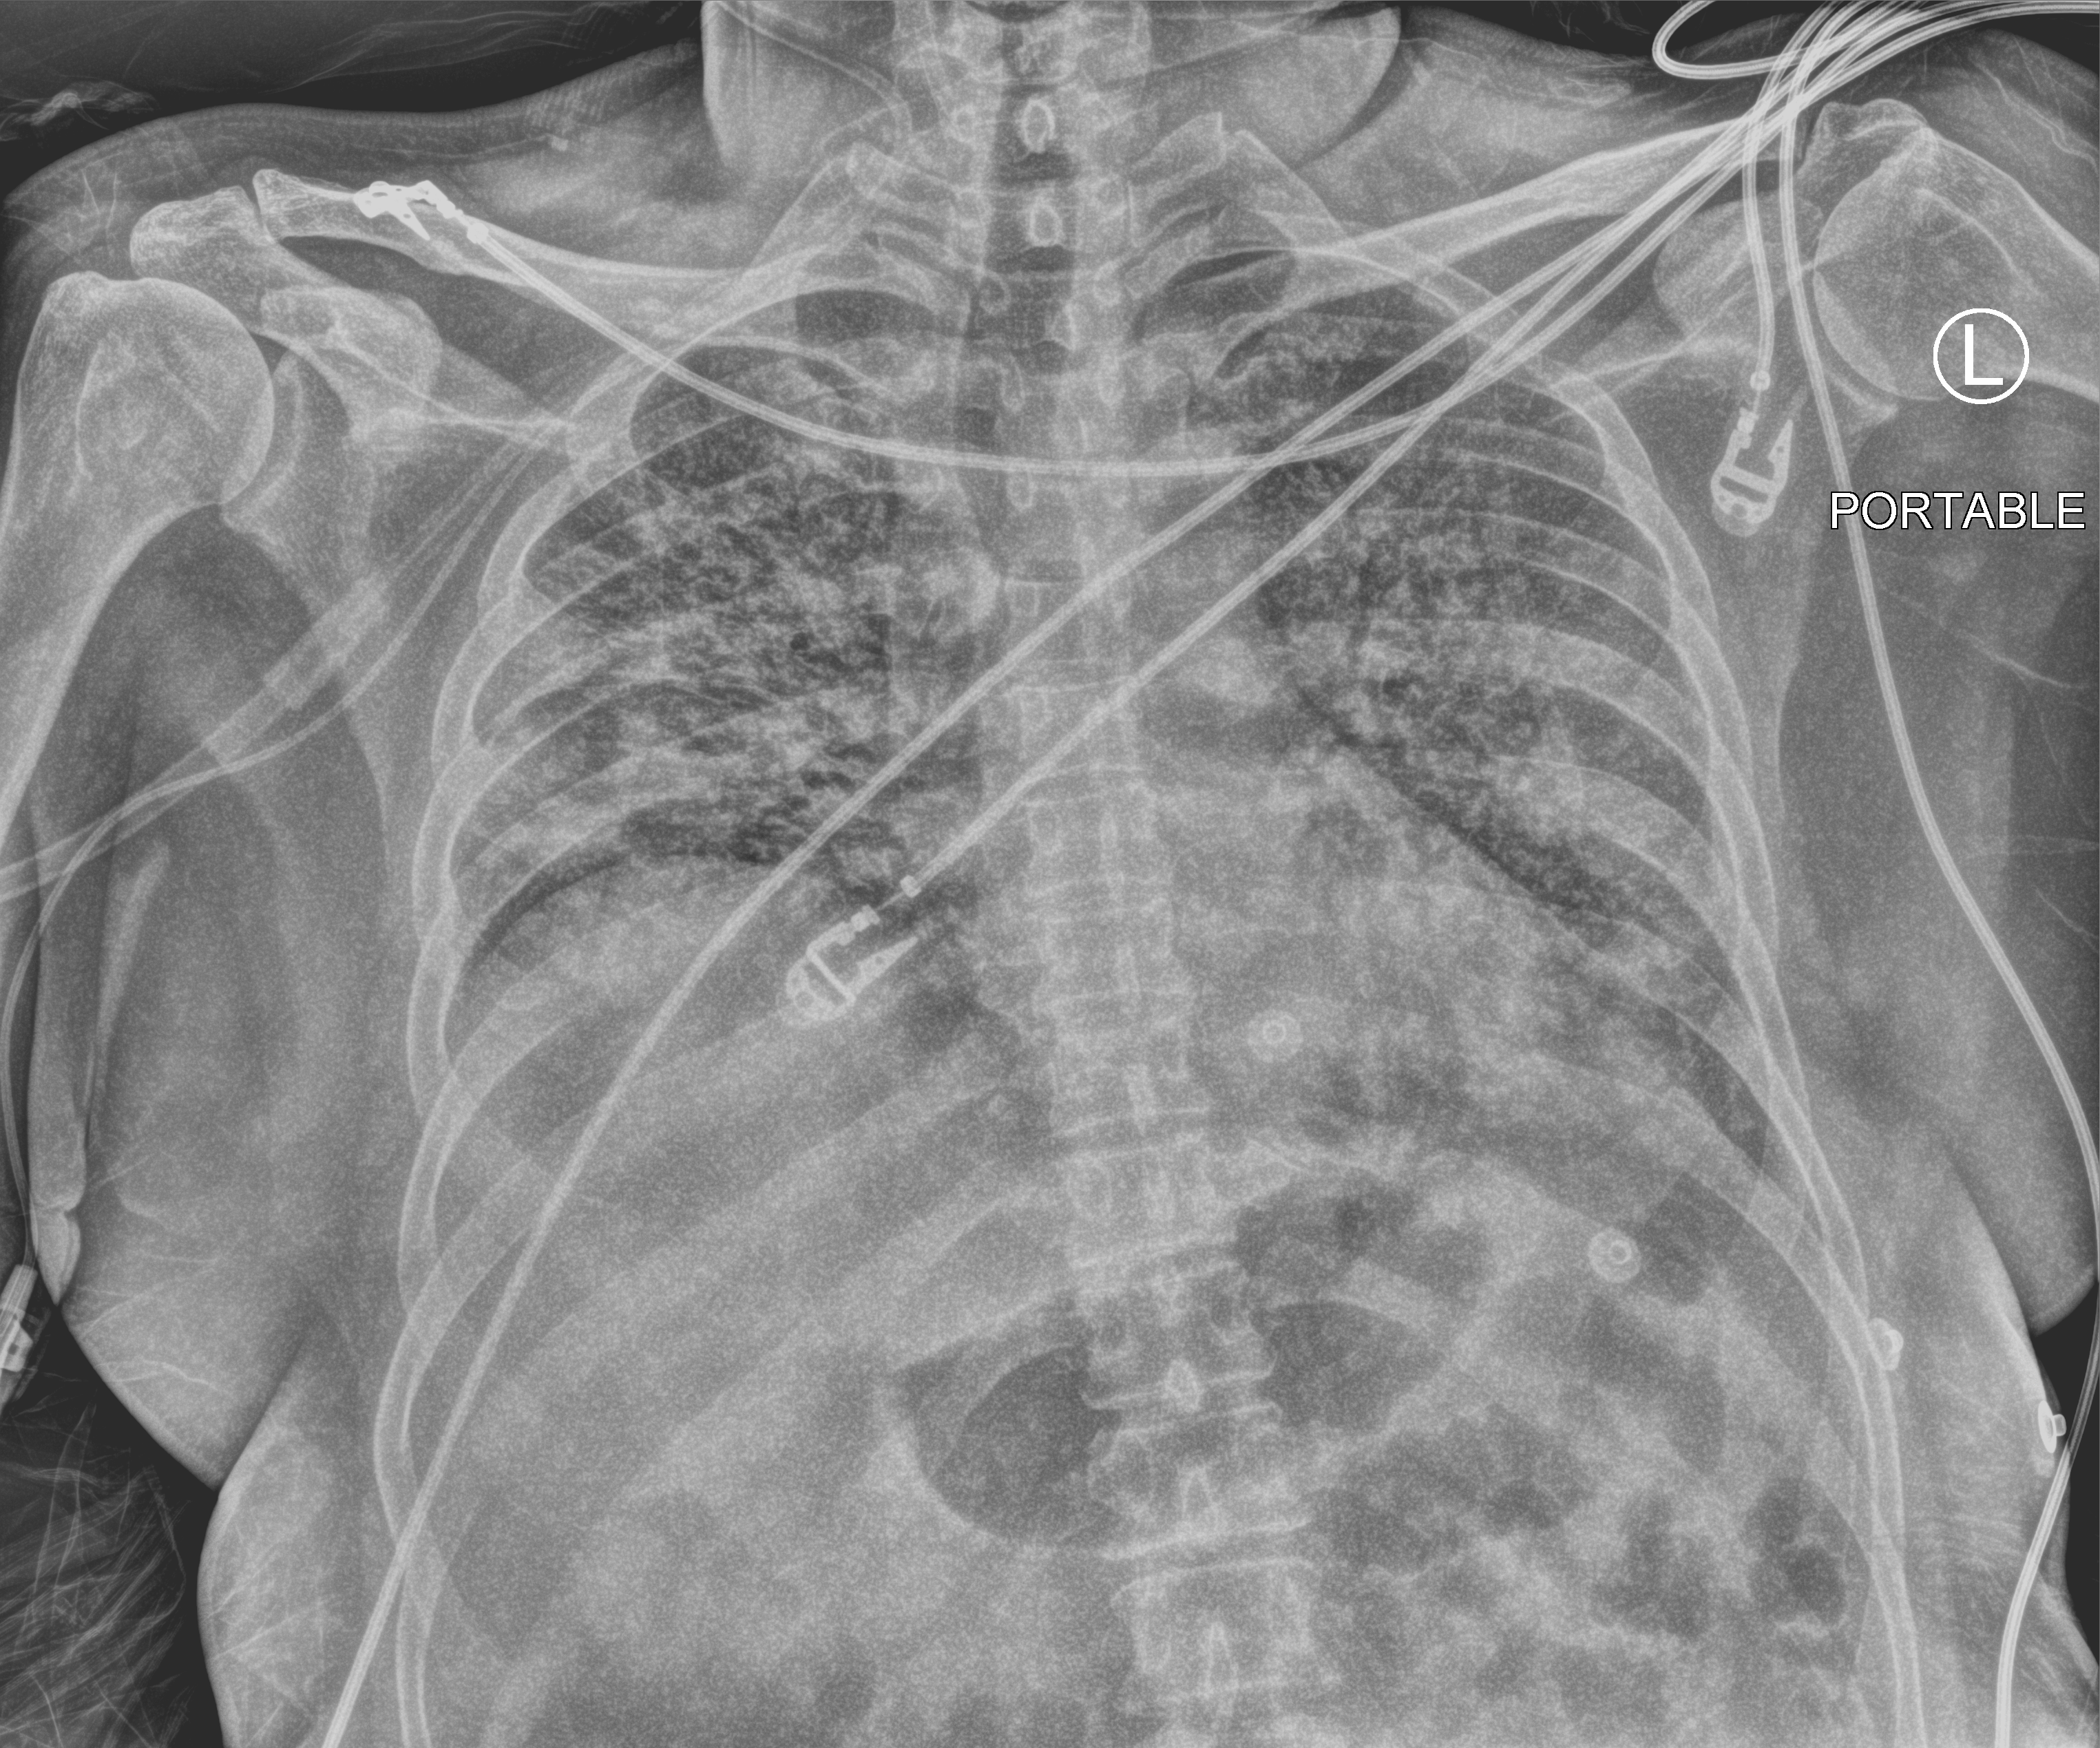
Bedside chest radiograph (computed radiography); anteroposterior (AP) projection. Male patient hospitalised with COVID-19, age 18–59 years.
From the hospital-stay record, not from the radiograph (when in the stay this image was taken is not recorded): admitted to intensive care during this hospital stay: yes.